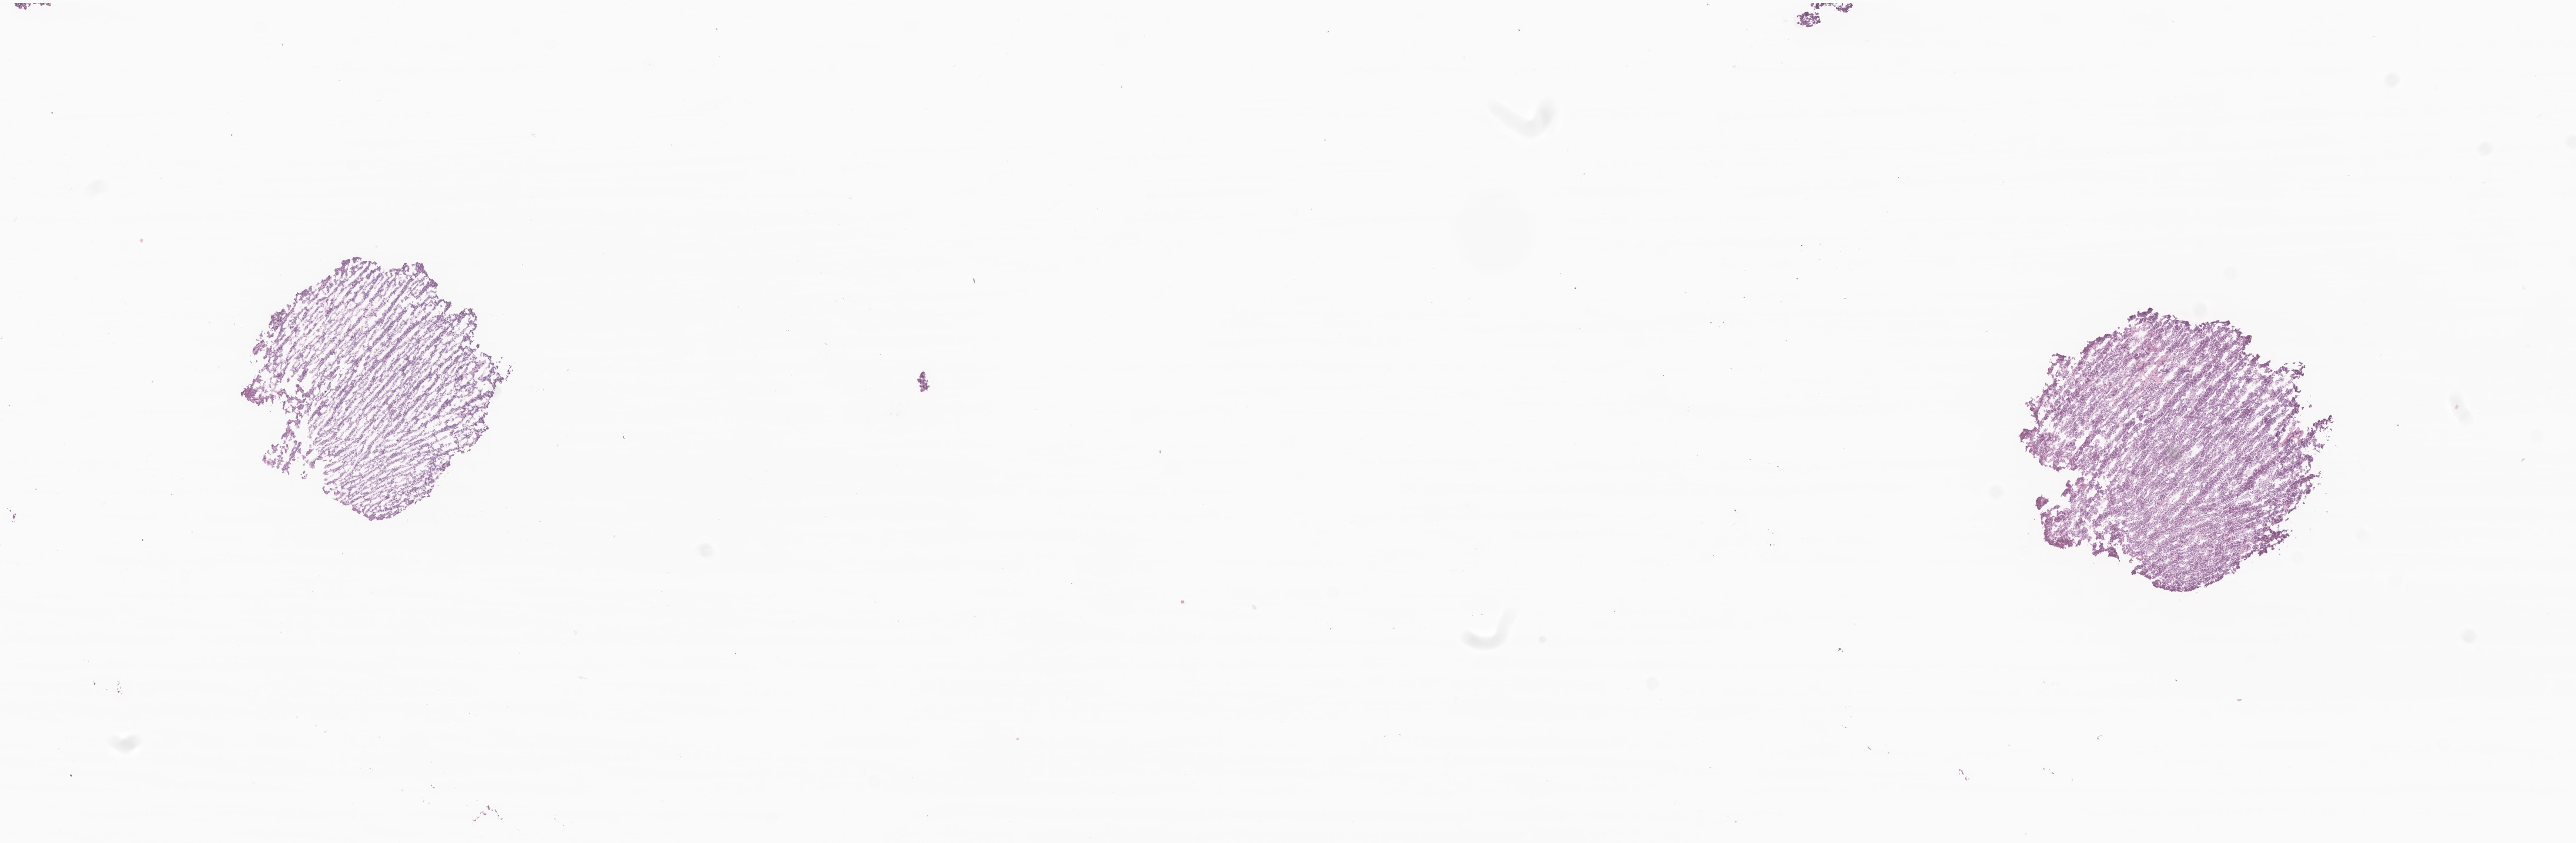
Digitized H&E-stained section of tumor tissue from the brain — low-resolution overview of the scanned area, about 18.5 x 6.0 mm. Cryosection (OCT / tissue freezing medium). Patient: female, age 86 months (7 years 2 months).
Diagnosis (ICD-O-3 morphology term): Medulloblastoma, NOS.